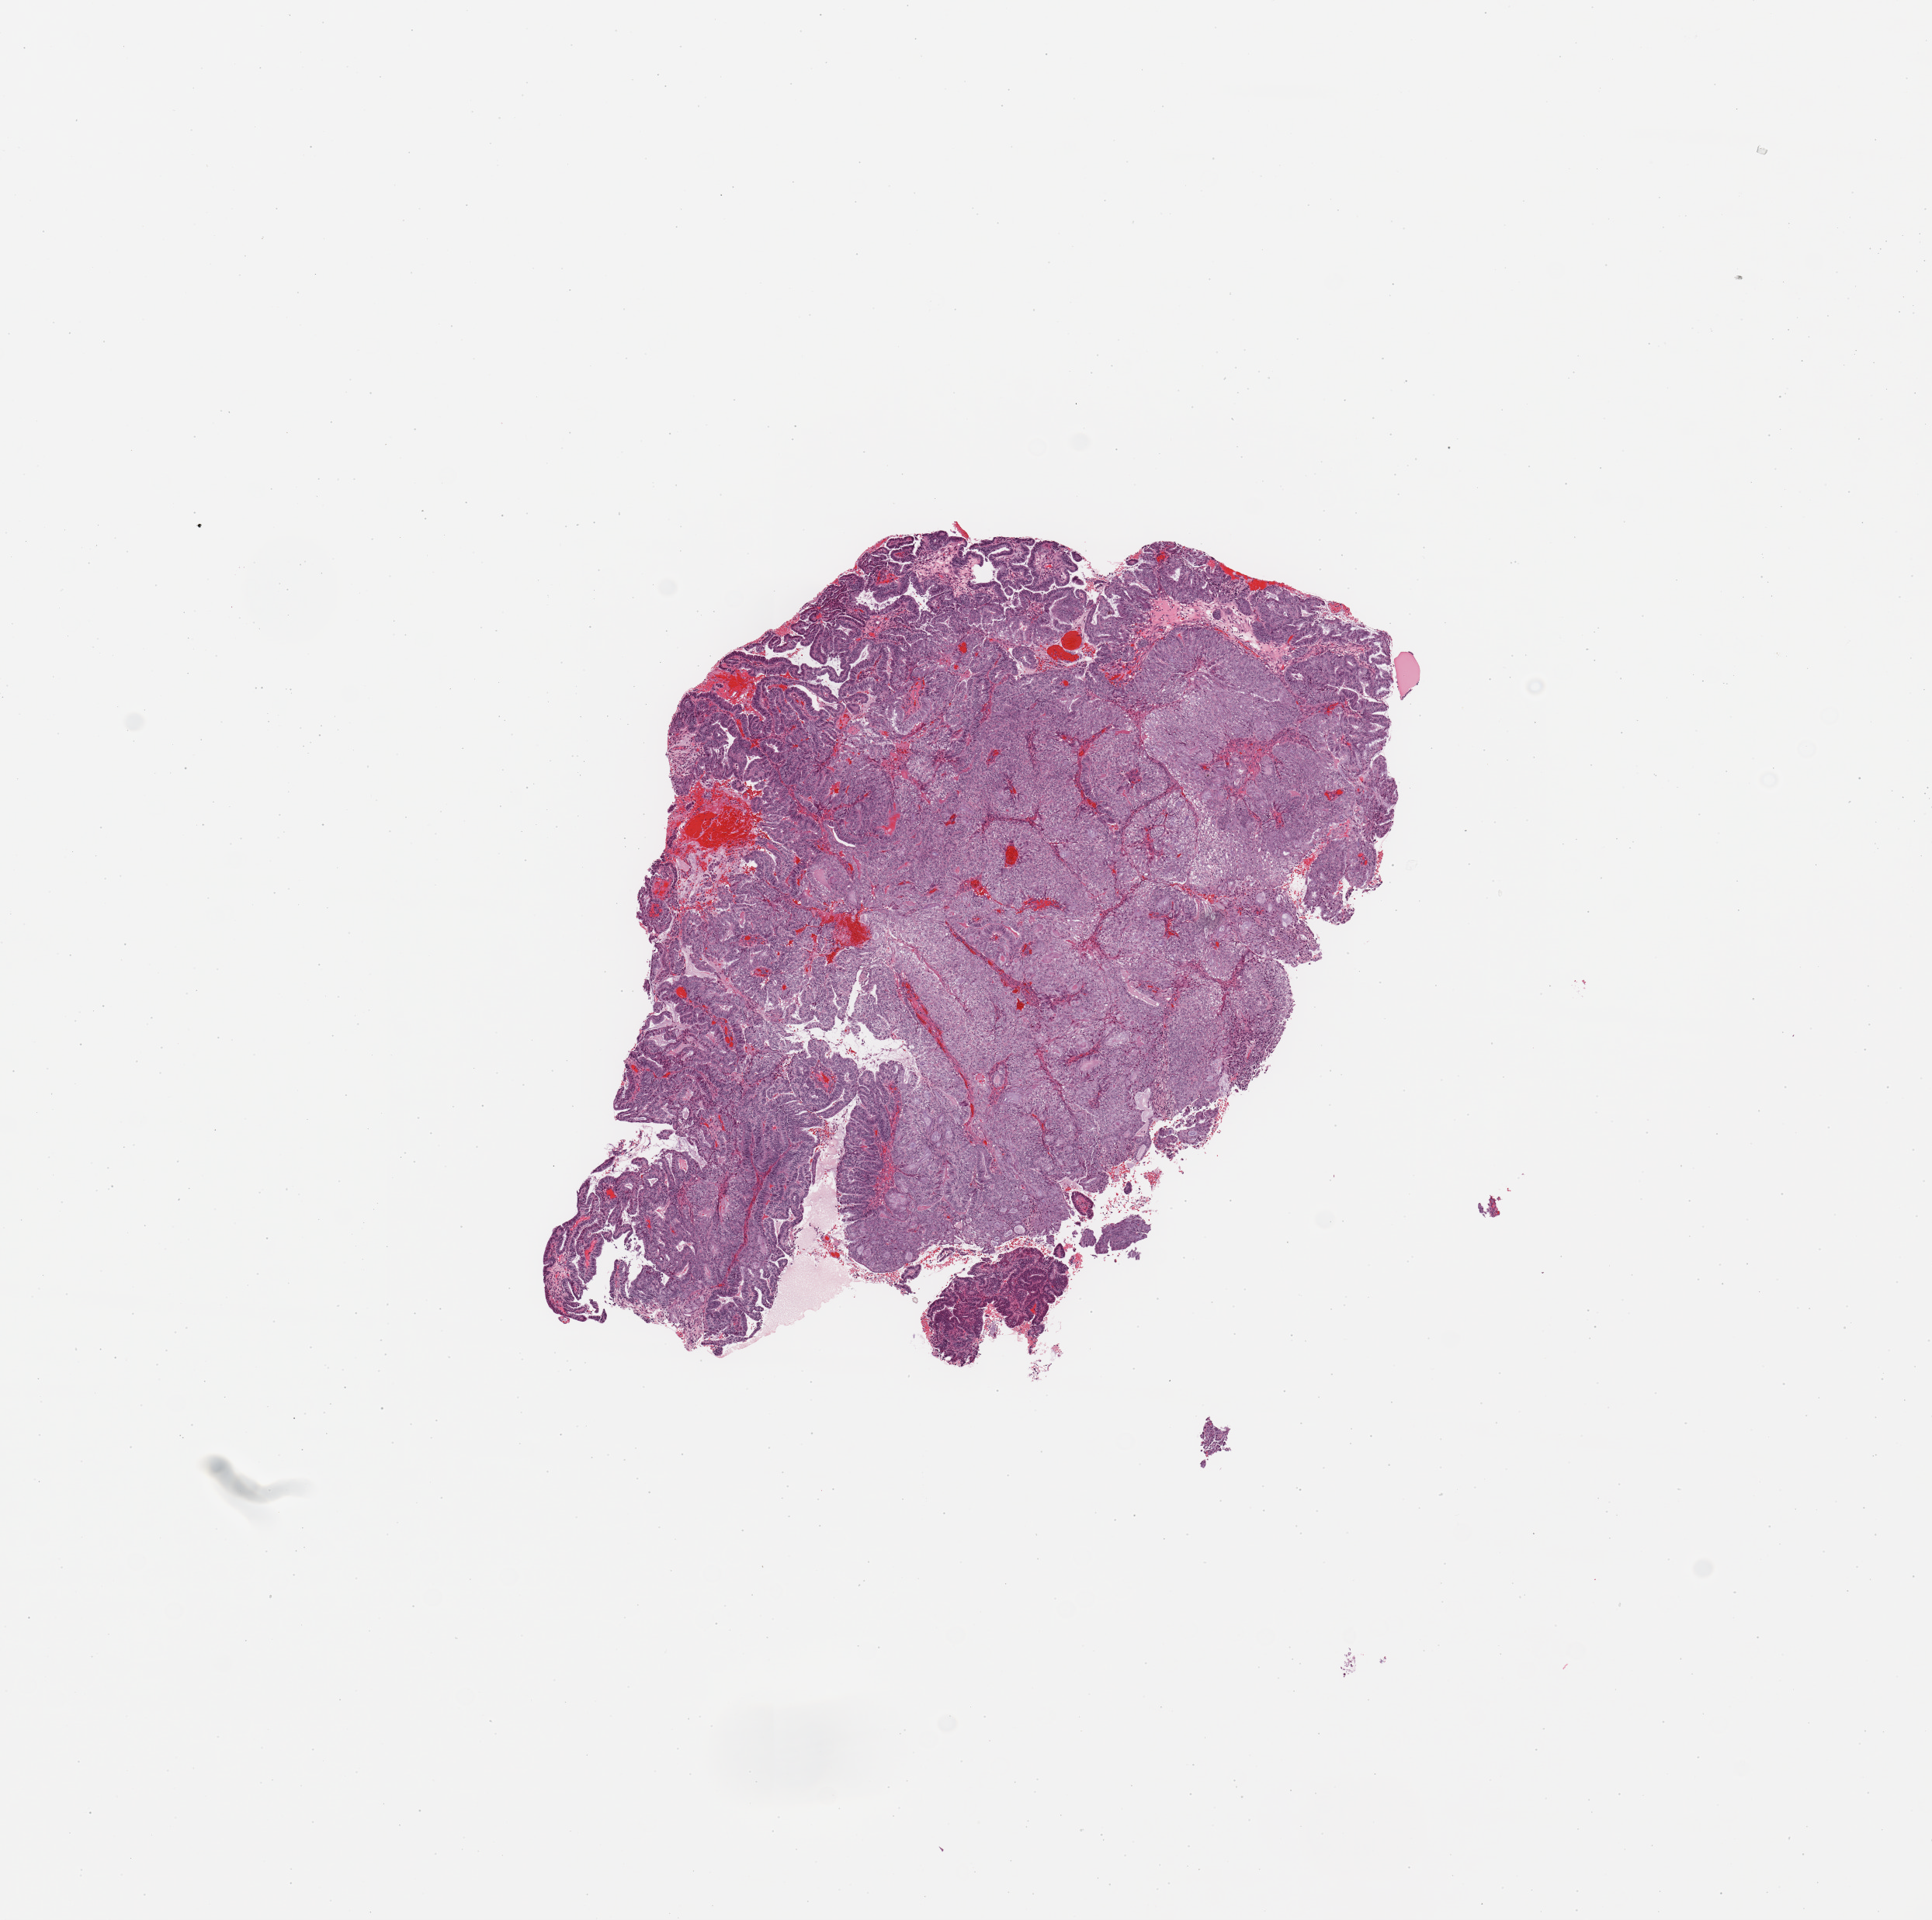
Whole-slide histology image, Hematoxylin and eosin (H&E) stained, shown as a low-resolution overview of the whole scanned area (about 9.8 x 9.8 mm, acquisition: 20x scan); tumour tissue sample, sampled site: uterus. Female, 80 y/o. Histologic grade: G2 (moderately differentiated). Composition of this section per pathologist review: tumour nuclei 90%, necrosis 0%.
AJCC pathologic stage: I. Diagnosis: Endometrioid adenocarcinoma, NOS.